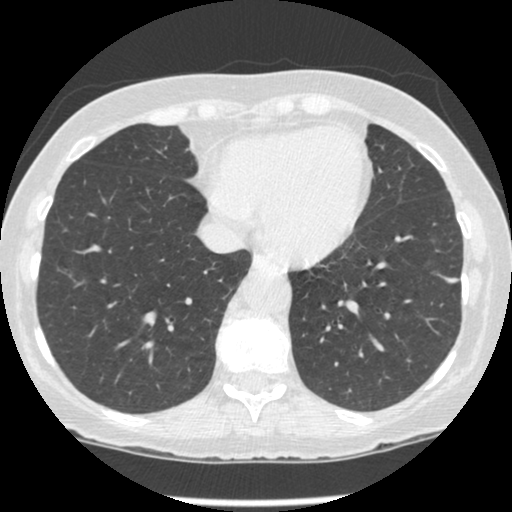
Low-dose screening chest CT, one axial slice; position 75 of 247 along the scan axis; reconstruction kernel STANDARD; lung window (W 1500 / L -600 HU); 1.25 mm slice thickness; 512 × 512 image matrix, field of view 303 × 303 mm.
Annotated regions visible in this slice (expert manual segmentation):
- lesion 1 (tumor, lower lobe of left lung): bounding box [x1, y1, x2, y2] px = [446, 277, 459, 283]